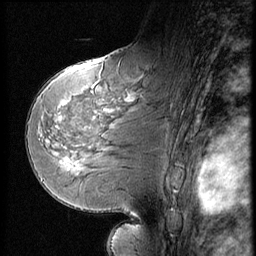
Breast MRI (dynamic contrast-enhanced), one sagittal slice; slice 32 of 56 in the series (ordered by position); dynamic contrast-enhanced series, image 2 of 3 at this slice position (ordered by acquisition); 1.5 T; TE 4.2 ms, TR 9 ms; 256 × 256 image matrix, field of view 180 × 180 mm. Patient: female, 58 years. Case-level facts recorded for this patient, not image findings: setting: breast cancer imaged before/during neoadjuvant chemotherapy; receptor status: HR-positive, HER2-negative.
Structures marked on this image (semi-automatically segmented with operator editing):
- analysis volume of interest (the breast-tissue region the enhancement analysis was run in; not a lesion): box from (x=51, y=147) to (x=96, y=185) px
- tumour enhancement mask (voxels above the 140 % enhancement threshold inside the analysis volume of interest): (x=62, y=160)–(x=80, y=165)